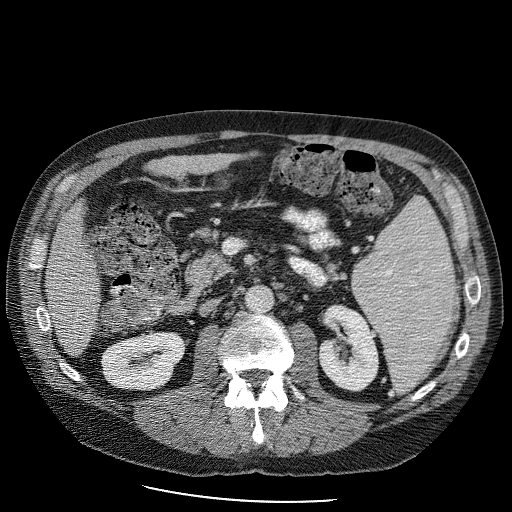
Contrast-enhanced abdominal CT (liver protocol), one axial slice. Reconstruction kernel STANDARD. 120 kVp. Soft-tissue window (W 400 / L 40 HU). 512 × 512 image matrix, field of view 400 × 400 mm. From the clinical record (not read from this slice): diagnosis: hepatocellular carcinoma (patient treated with transarterial chemoembolisation; whether this scan precedes or follows treatment is not stated here); TNM stage (as recorded): Stage-II; Child-Pugh class: B.
Outlined on this slice (semi-automatic segmentation, software-assisted and operator-edited):
- liver parenchyma outside the tumour (the mass and vessels are separate outlines, so this box may not span the whole liver): bounding box (x1, y1, x2, y2) in pixels: (44, 142, 270, 352)
- liver vessels: (80, 302, 83, 305)